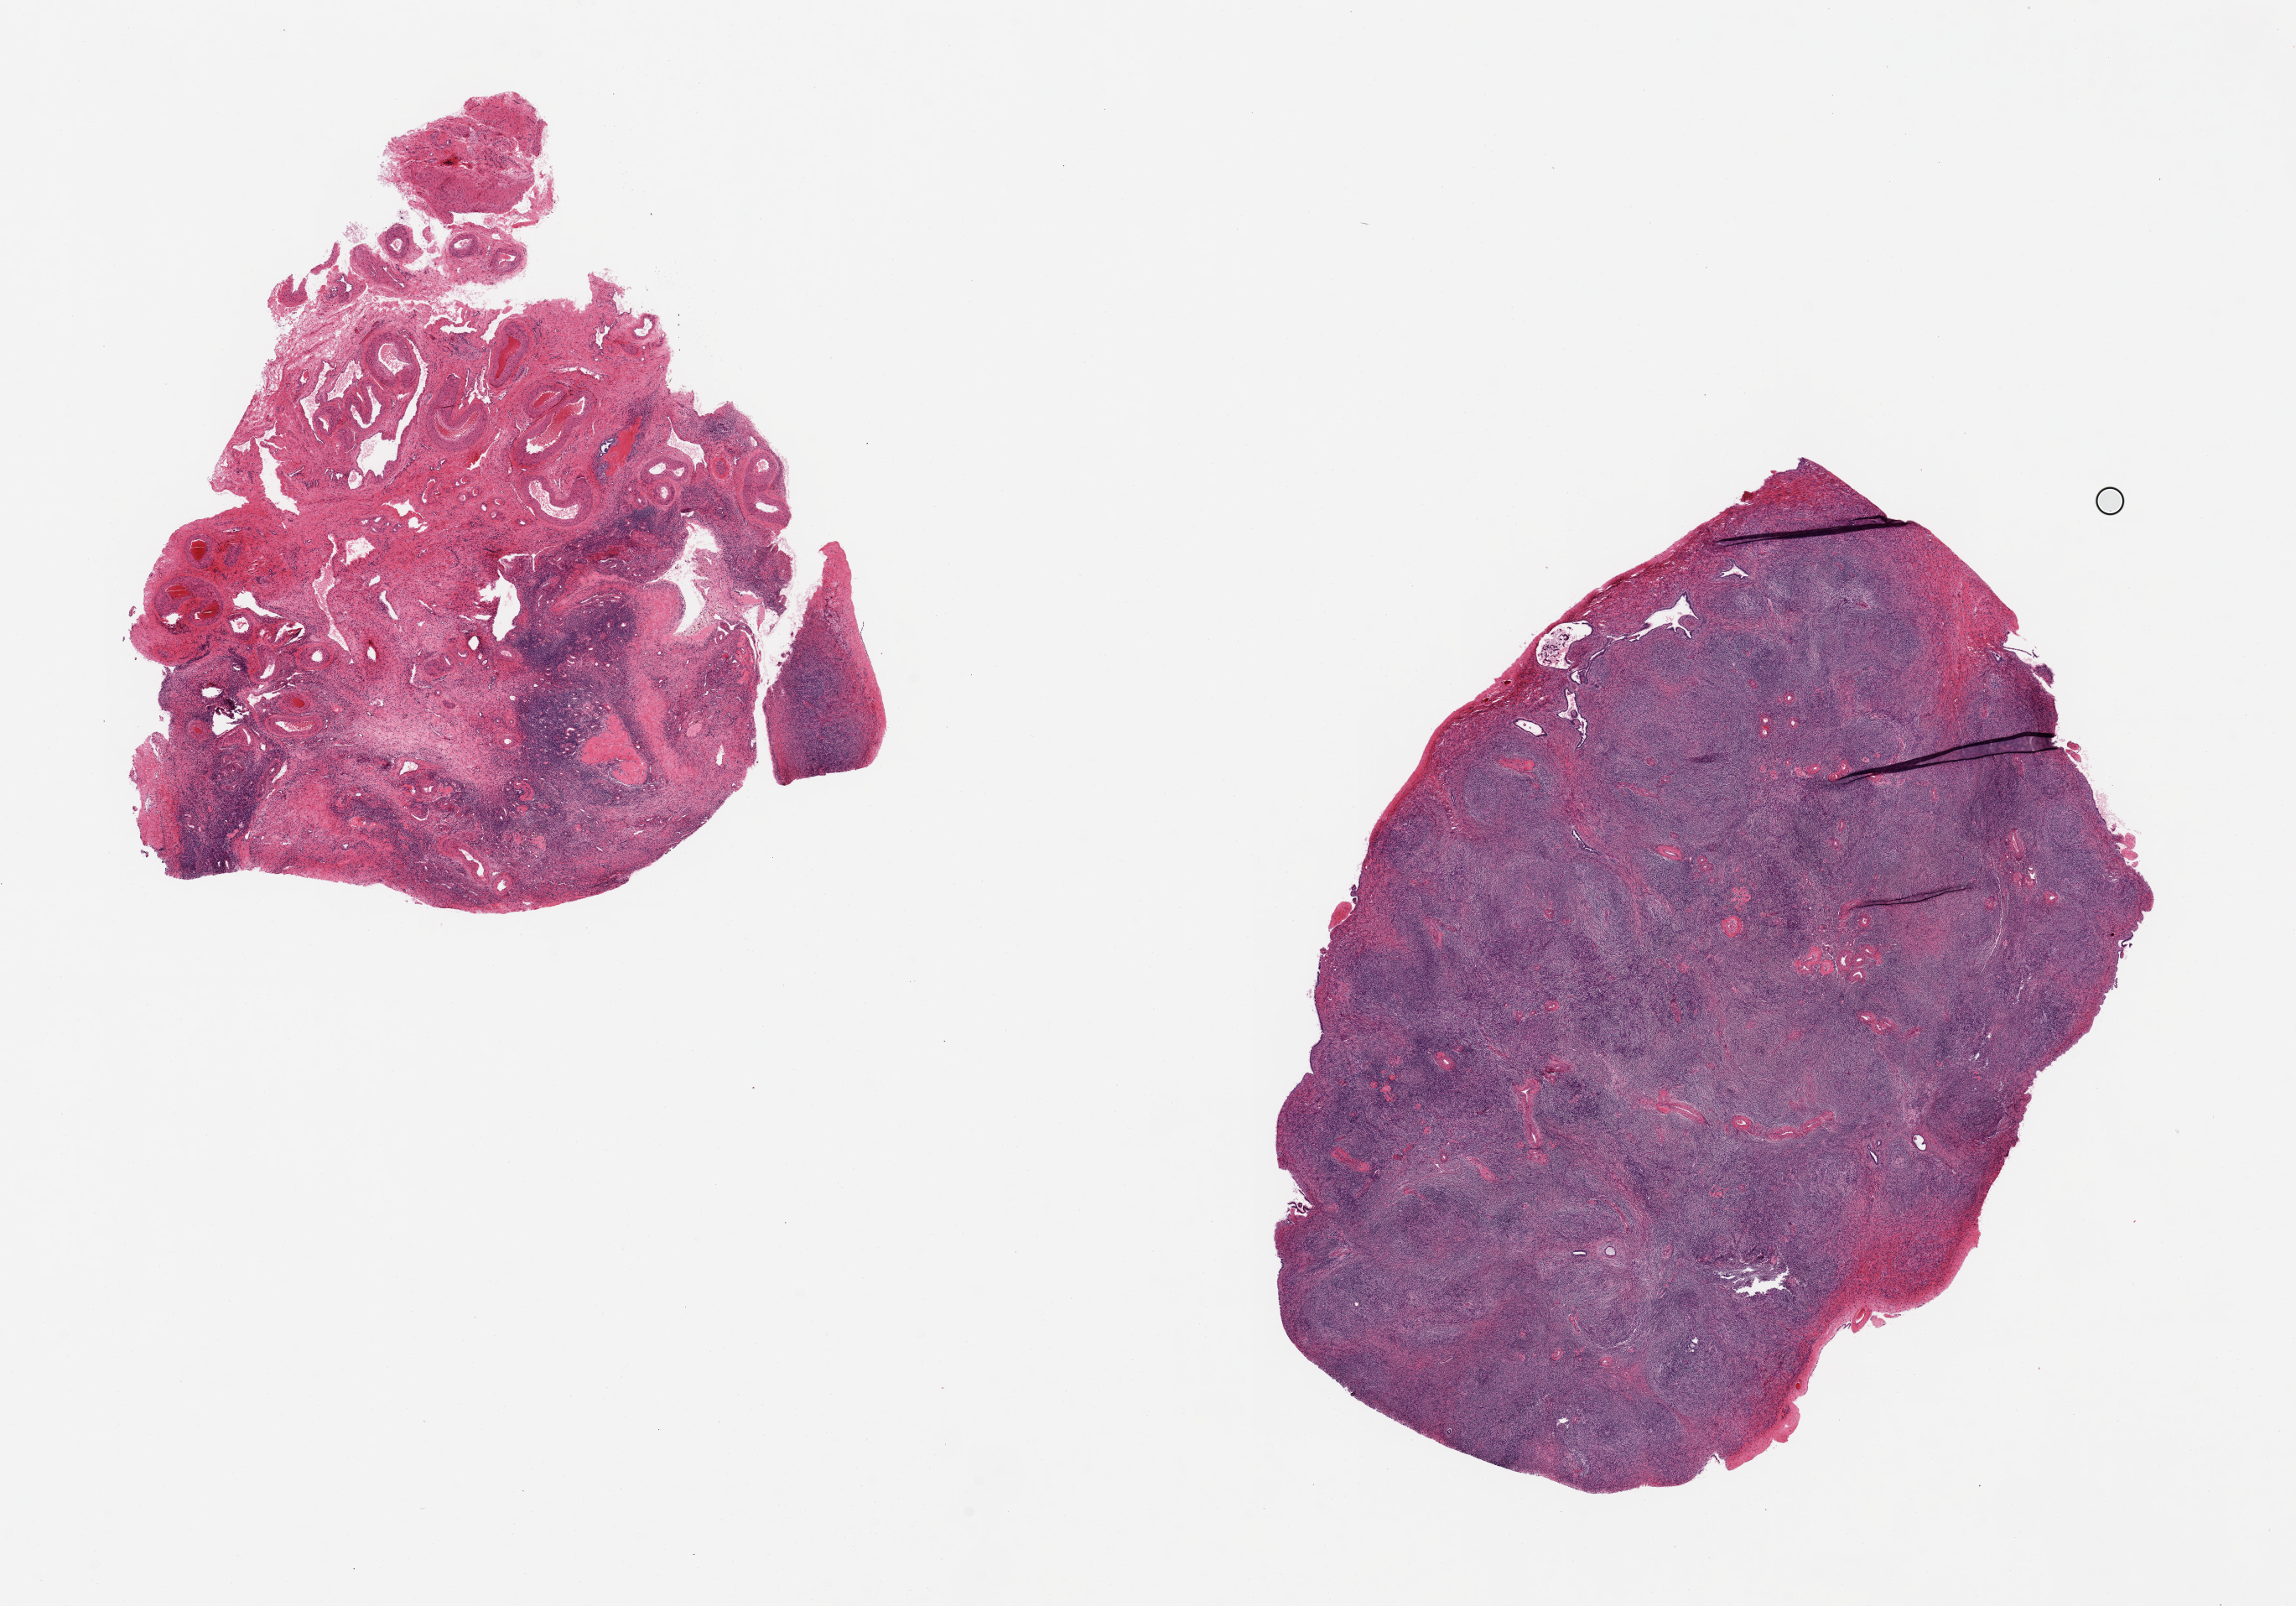
Whole-slide image, hematoxylin and eosin (H&E) stain, brightfield — shown as a low-resolution overview of the whole scanned area (about 21.7 x 15.1 mm, acquisition: 20x scan), PAXgene-fixed paraffin-embedded (PFPE) section, target tissue: ovary, donor tissue sample. Donor: female.
Reviewer comment on this tissue sample: 2 pieces, 7.5x7 & 10x7mm; post menopausal atrophy; one all stroma, the other ~60% hilum, dlineated.